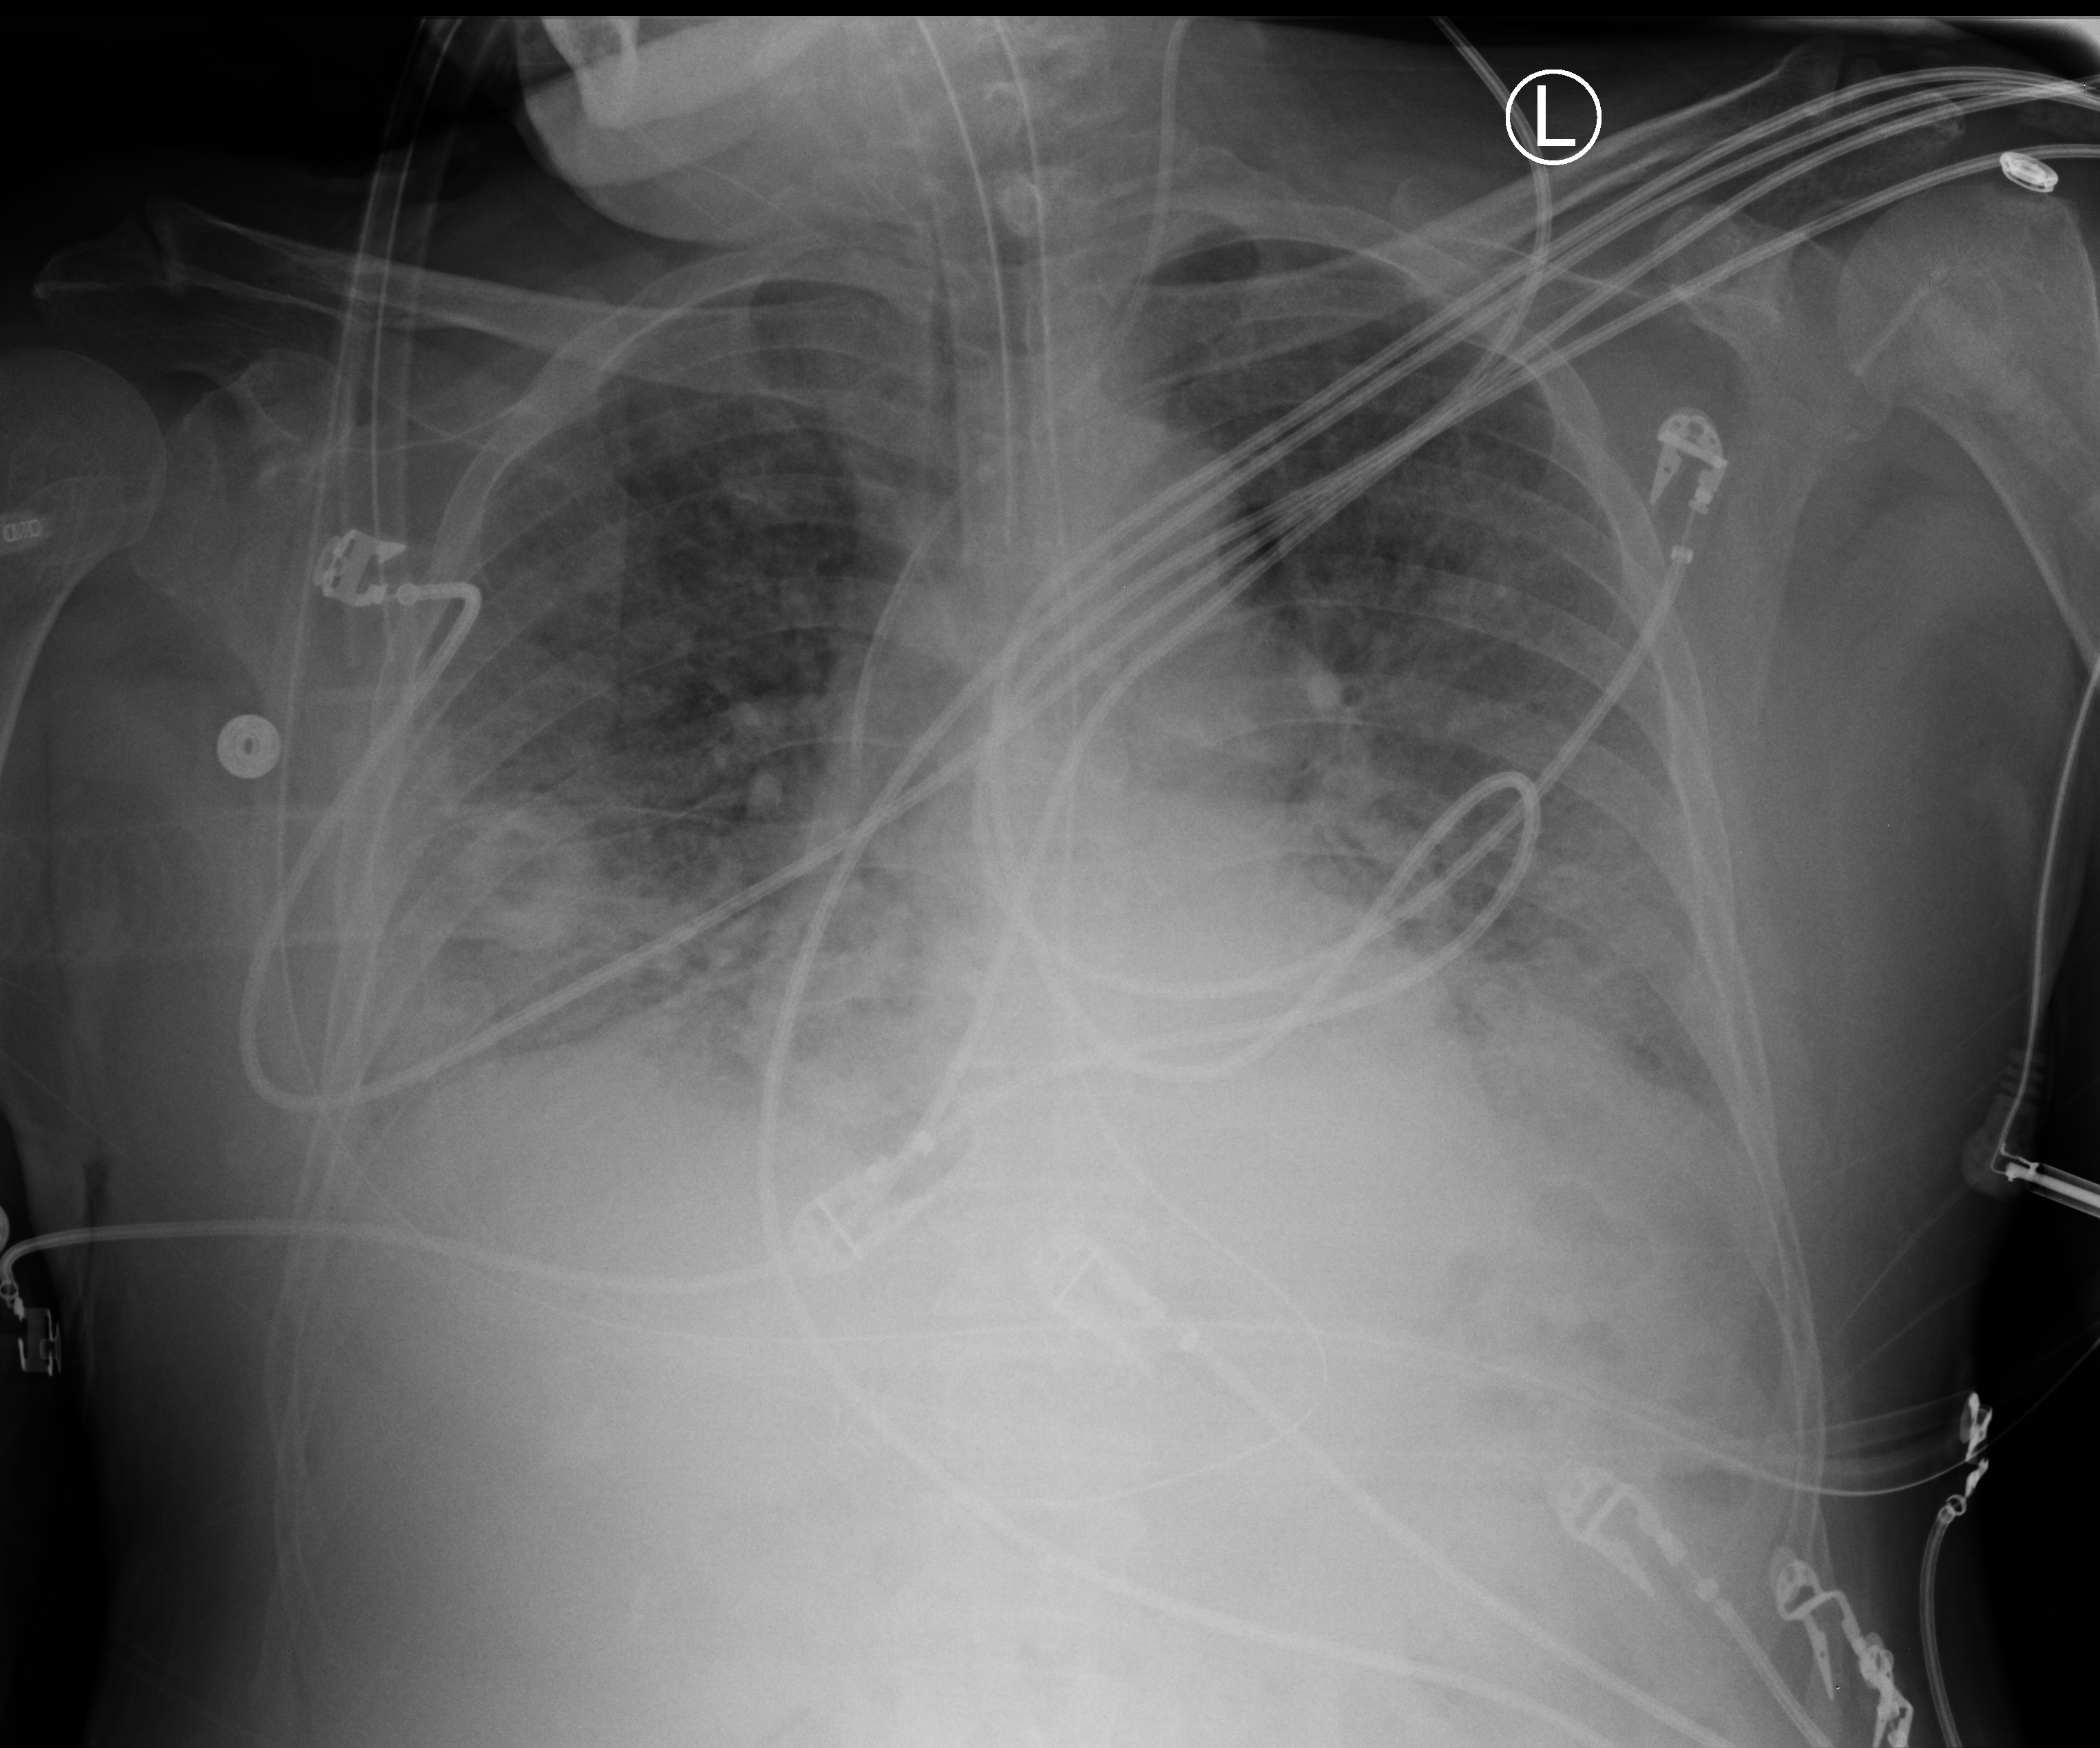
Bedside chest radiograph (computed radiography), anteroposterior (AP) projection. Patient hospitalised with COVID-19; male, aged 60–74 years.
Admission-level facts for this patient (not findings on this image; timing relative to this image not recorded): hypertension (admission record): no.